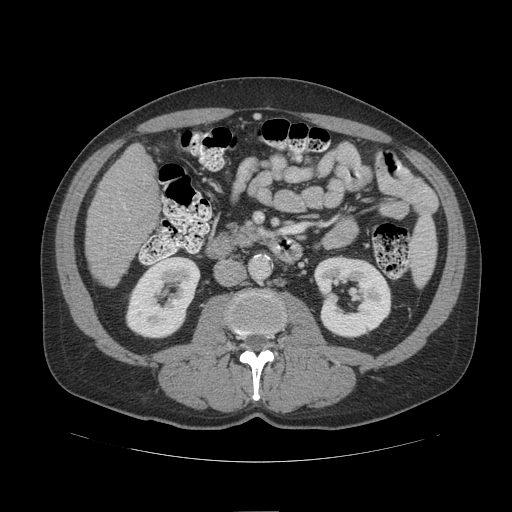
Contrast-enhanced abdominal CT (liver protocol), one axial slice. Position 36 of 109 along the scan axis. 140 kVp. Soft-tissue window (W 400 / L 40 HU). 2.5 mm slice thickness. 512 × 512 image matrix, field of view 420 × 420 mm. Case-level facts recorded for this patient, not image findings: diagnosis: hepatocellular carcinoma (patient treated with transarterial chemoembolisation; whether this scan precedes or follows treatment is not stated here); TNM stage (as recorded): Stage-IIIB; Child-Pugh class: A; tumour differentiation: poorly differentiated.
Structures marked on this image (semi-automatically segmented with operator editing):
- liver parenchyma outside the tumour (the mass and vessels are separate outlines, so this box may not span the whole liver): box from (x=86, y=144) to (x=158, y=286) px